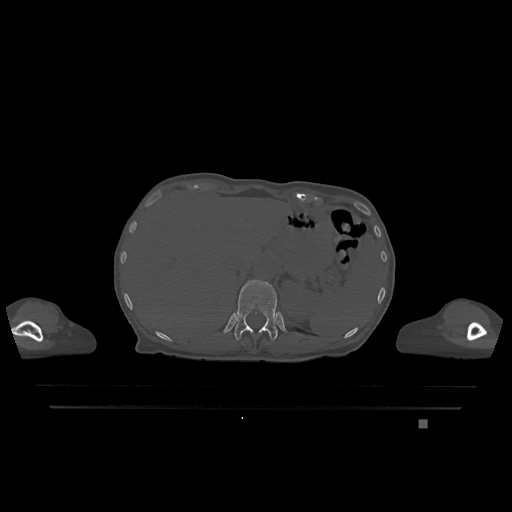
CT including the spine, one axial slice. Slice 542 of 1317 in the series (ordered by position). Bone window (W 1800 / L 400 HU). 0.5 mm slice thickness. 512 × 512 image matrix. Patient: female, 74 years. Case-level facts recorded for this patient, not image findings: primary cancer: lung; vertebrae with lytic lesions (as recorded): T1, T4, T5, T6, L4, L5.
Annotated regions visible in this slice (semi-automatically segmented with operator editing):
- T12 vertebra: bounding box <234,280,278,341> (left, top, right, bottom; pixels)